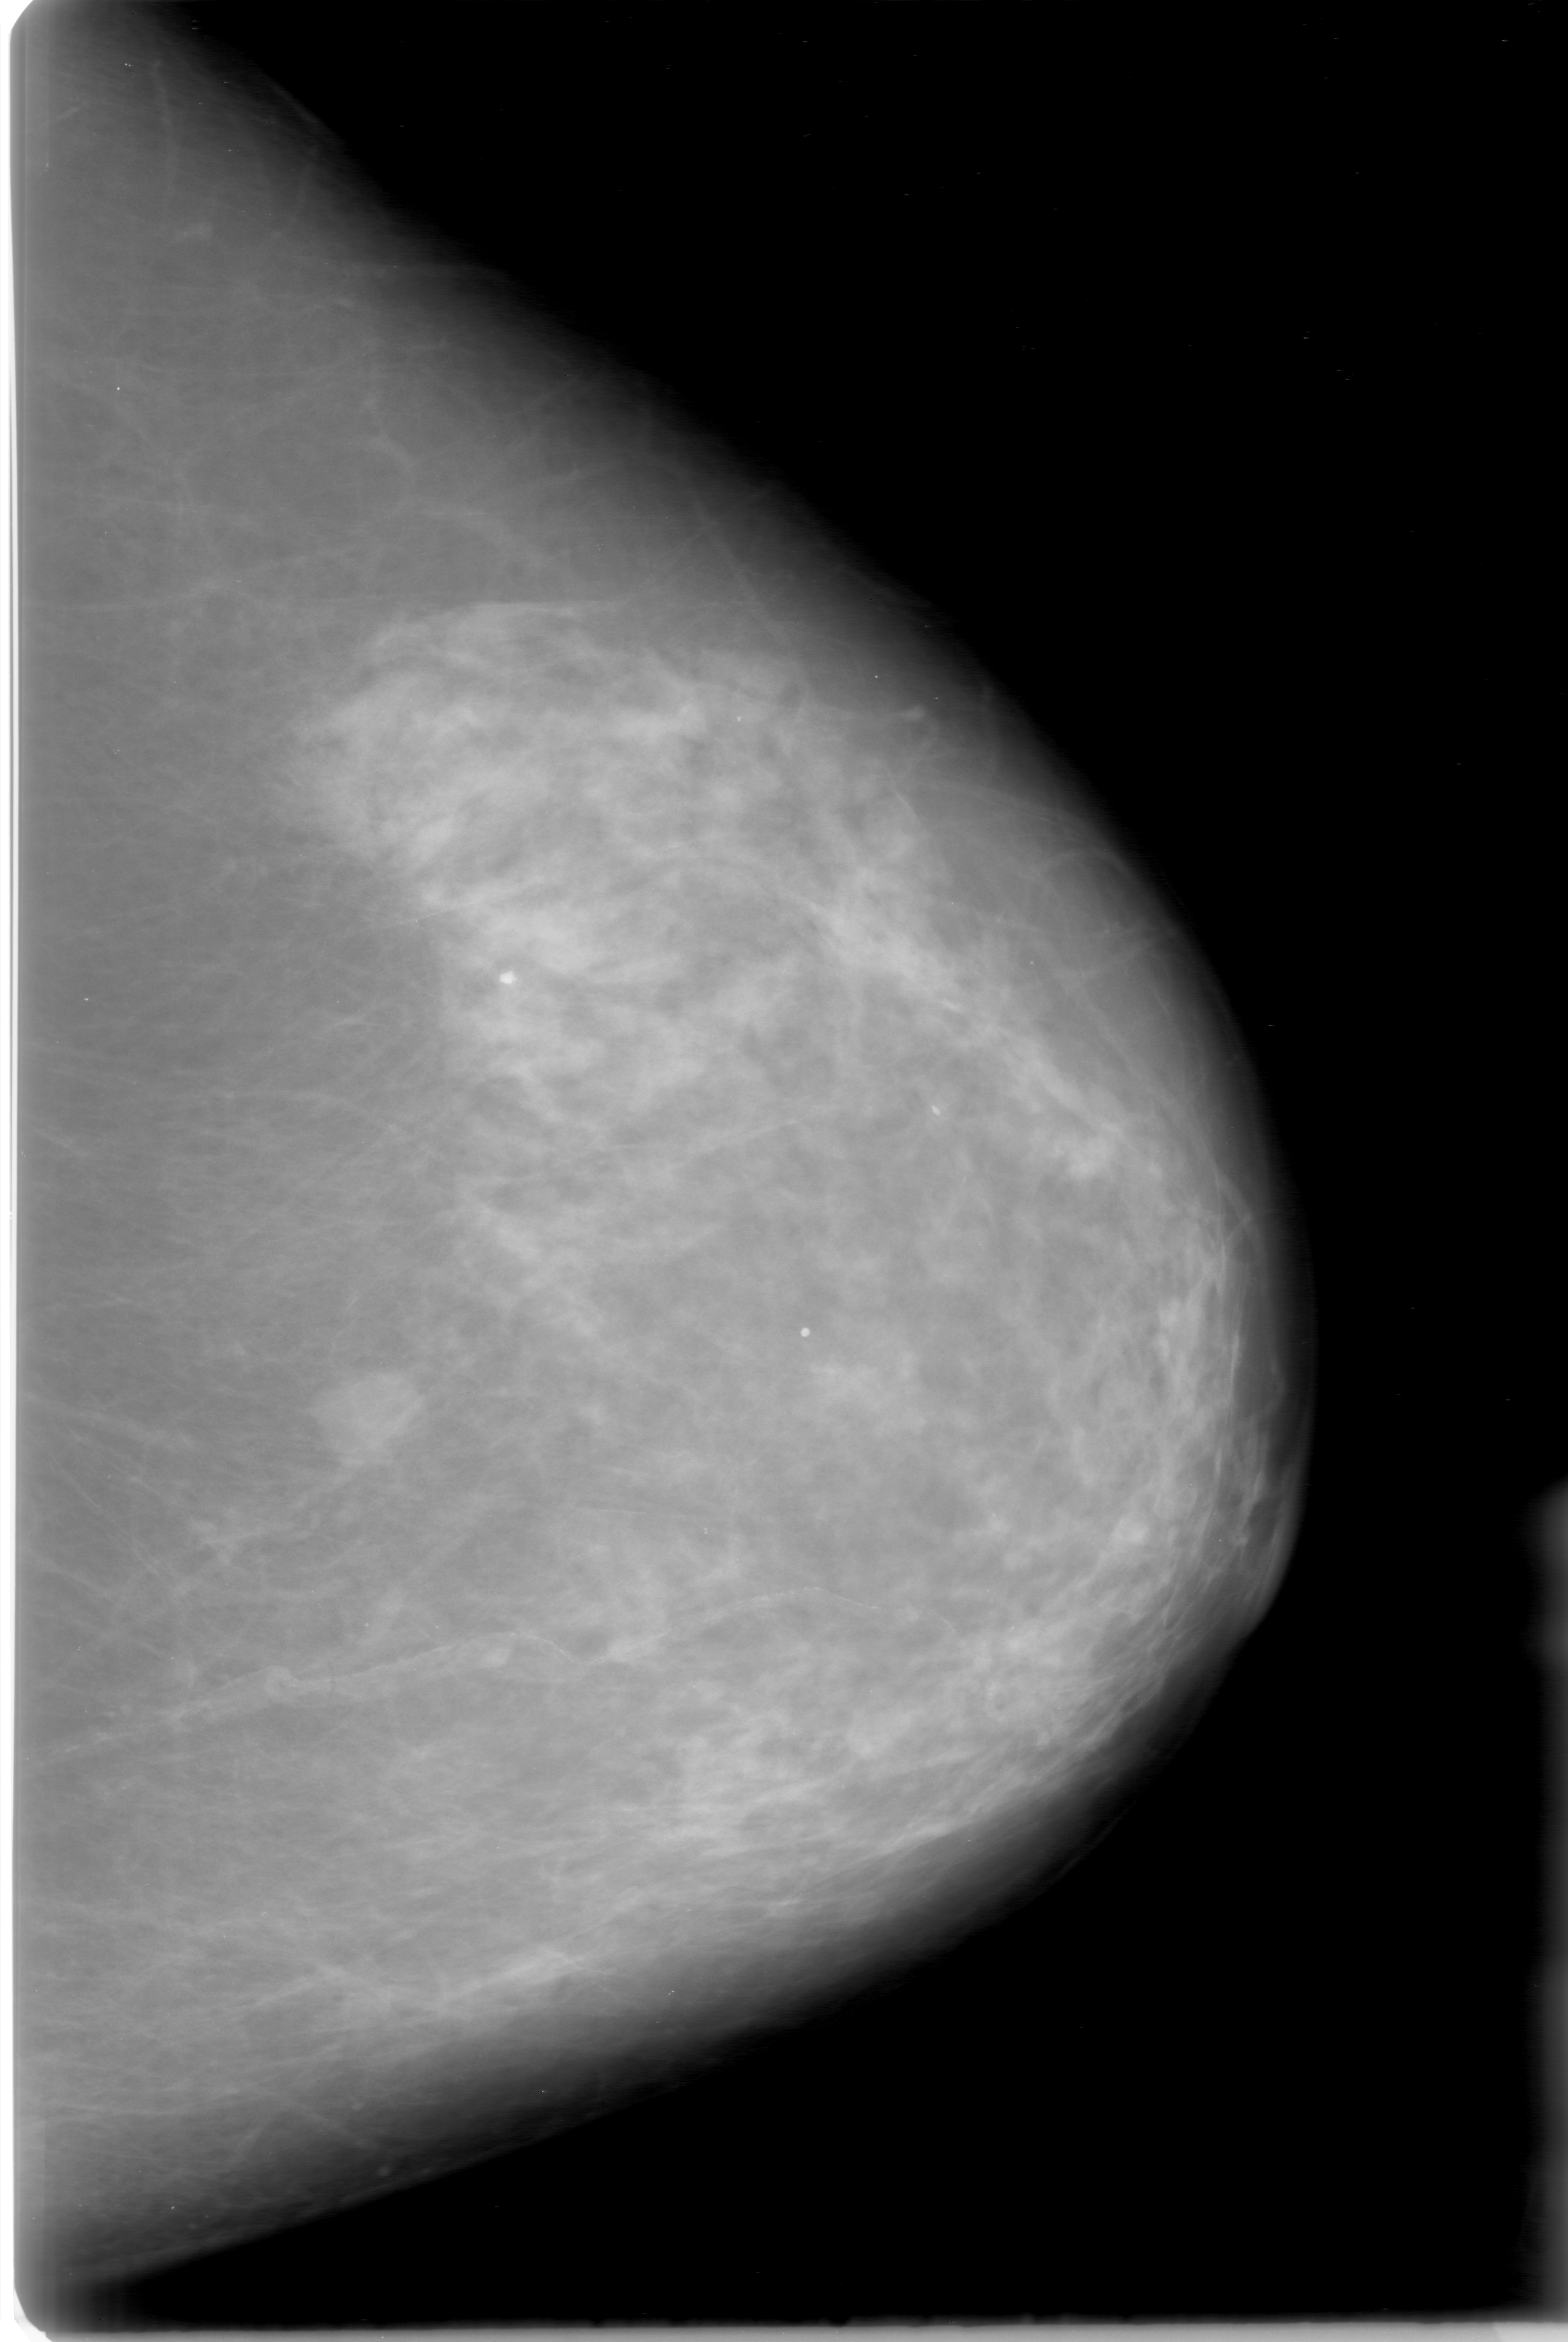
Digitized screen-film mammogram, left breast, CC view, BI-RADS breast density category 3 (scale 1–4).
Abnormality record for this image: mass, shape lobulated, margins obscured; BI-RADS assessment category 0 (incomplete: needs additional imaging); subtlety rating 5 on a 1 (subtle) to 5 (obvious) scale; pathology (as recorded): benign.